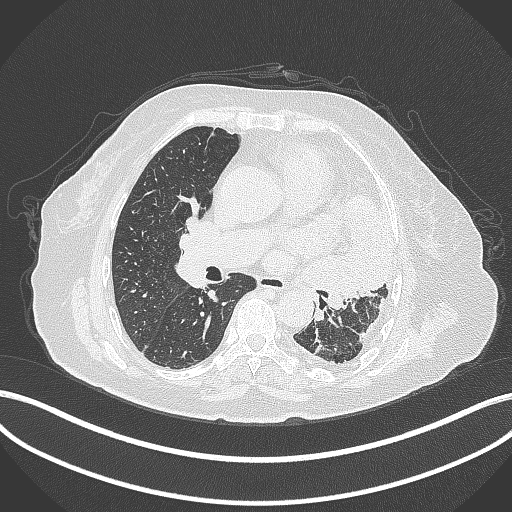
Chest CT, one axial slice; position 197 of 399 along the scan axis; reconstruction kernel B70f; lung window (W 1500 / L -600 HU); 1 mm slice thickness; 512 × 512 image matrix, field of view 400 × 400 mm. Female patient, age 75 years. Case-level facts recorded for this patient, not image findings: clinical TNM (as recorded): T3 N3 M1.
Annotated regions visible in this slice (rectangle marked by the reading radiologist):
- lung tumour (recorded histology: adenocarcinoma): bounding box (x1, y1, x2, y2) in pixels: (298, 192, 393, 319)